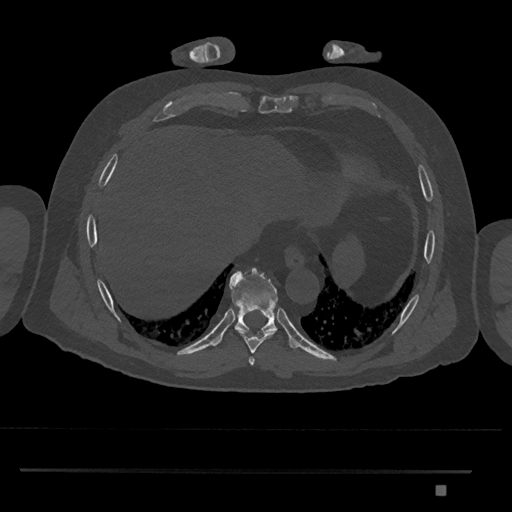
CT including the spine, one axial slice. Slice 1083 of 1134 in the series (ordered by position). 120 kVp. Bone window (W 1800 / L 400 HU). 0.5 mm slice thickness. 512 × 512 image matrix, field of view 429 × 429 mm. Male patient, age 65 years. From the clinical record (not read from this slice): primary cancer: prostate.
Outlined on this slice (semi-automatic segmentation, software-assisted and operator-edited):
- T8 vertebra: box from (x=235, y=329) to (x=276, y=353) px
- T9 vertebra: (x=230, y=268)–(x=278, y=334)